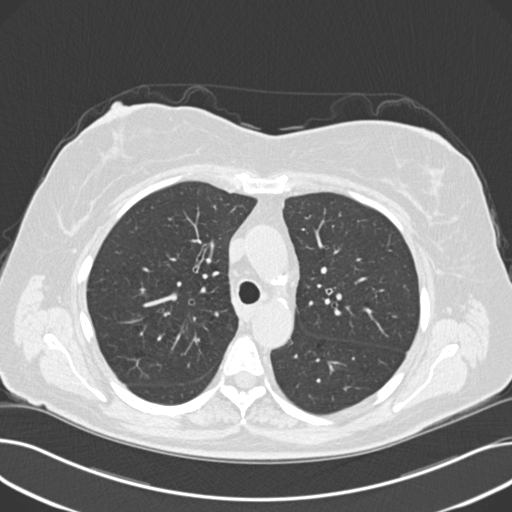
Chest CT (low-dose screening protocol), one axial image. Third screening round (two years after baseline). Lung window (W 1500 / L -600 HU). 2 mm slice thickness. Standard (soft-tissue) reconstruction kernel (B30f). 512 × 512 image matrix. Female participant, aged 60 years at enrolment. Current smoker at enrolment.
• Expert reader's lesion annotation, box from (x=312, y=224) to (x=363, y=270) px.
• The screening reader recorded 8 non-calcified nodules or masses ≥4 mm on this exam (right upper lobe, lingula, lingula, right middle lobe, right lower lobe, left lower lobe, left lower lobe, left lower lobe); which of them this box marks is not recorded.